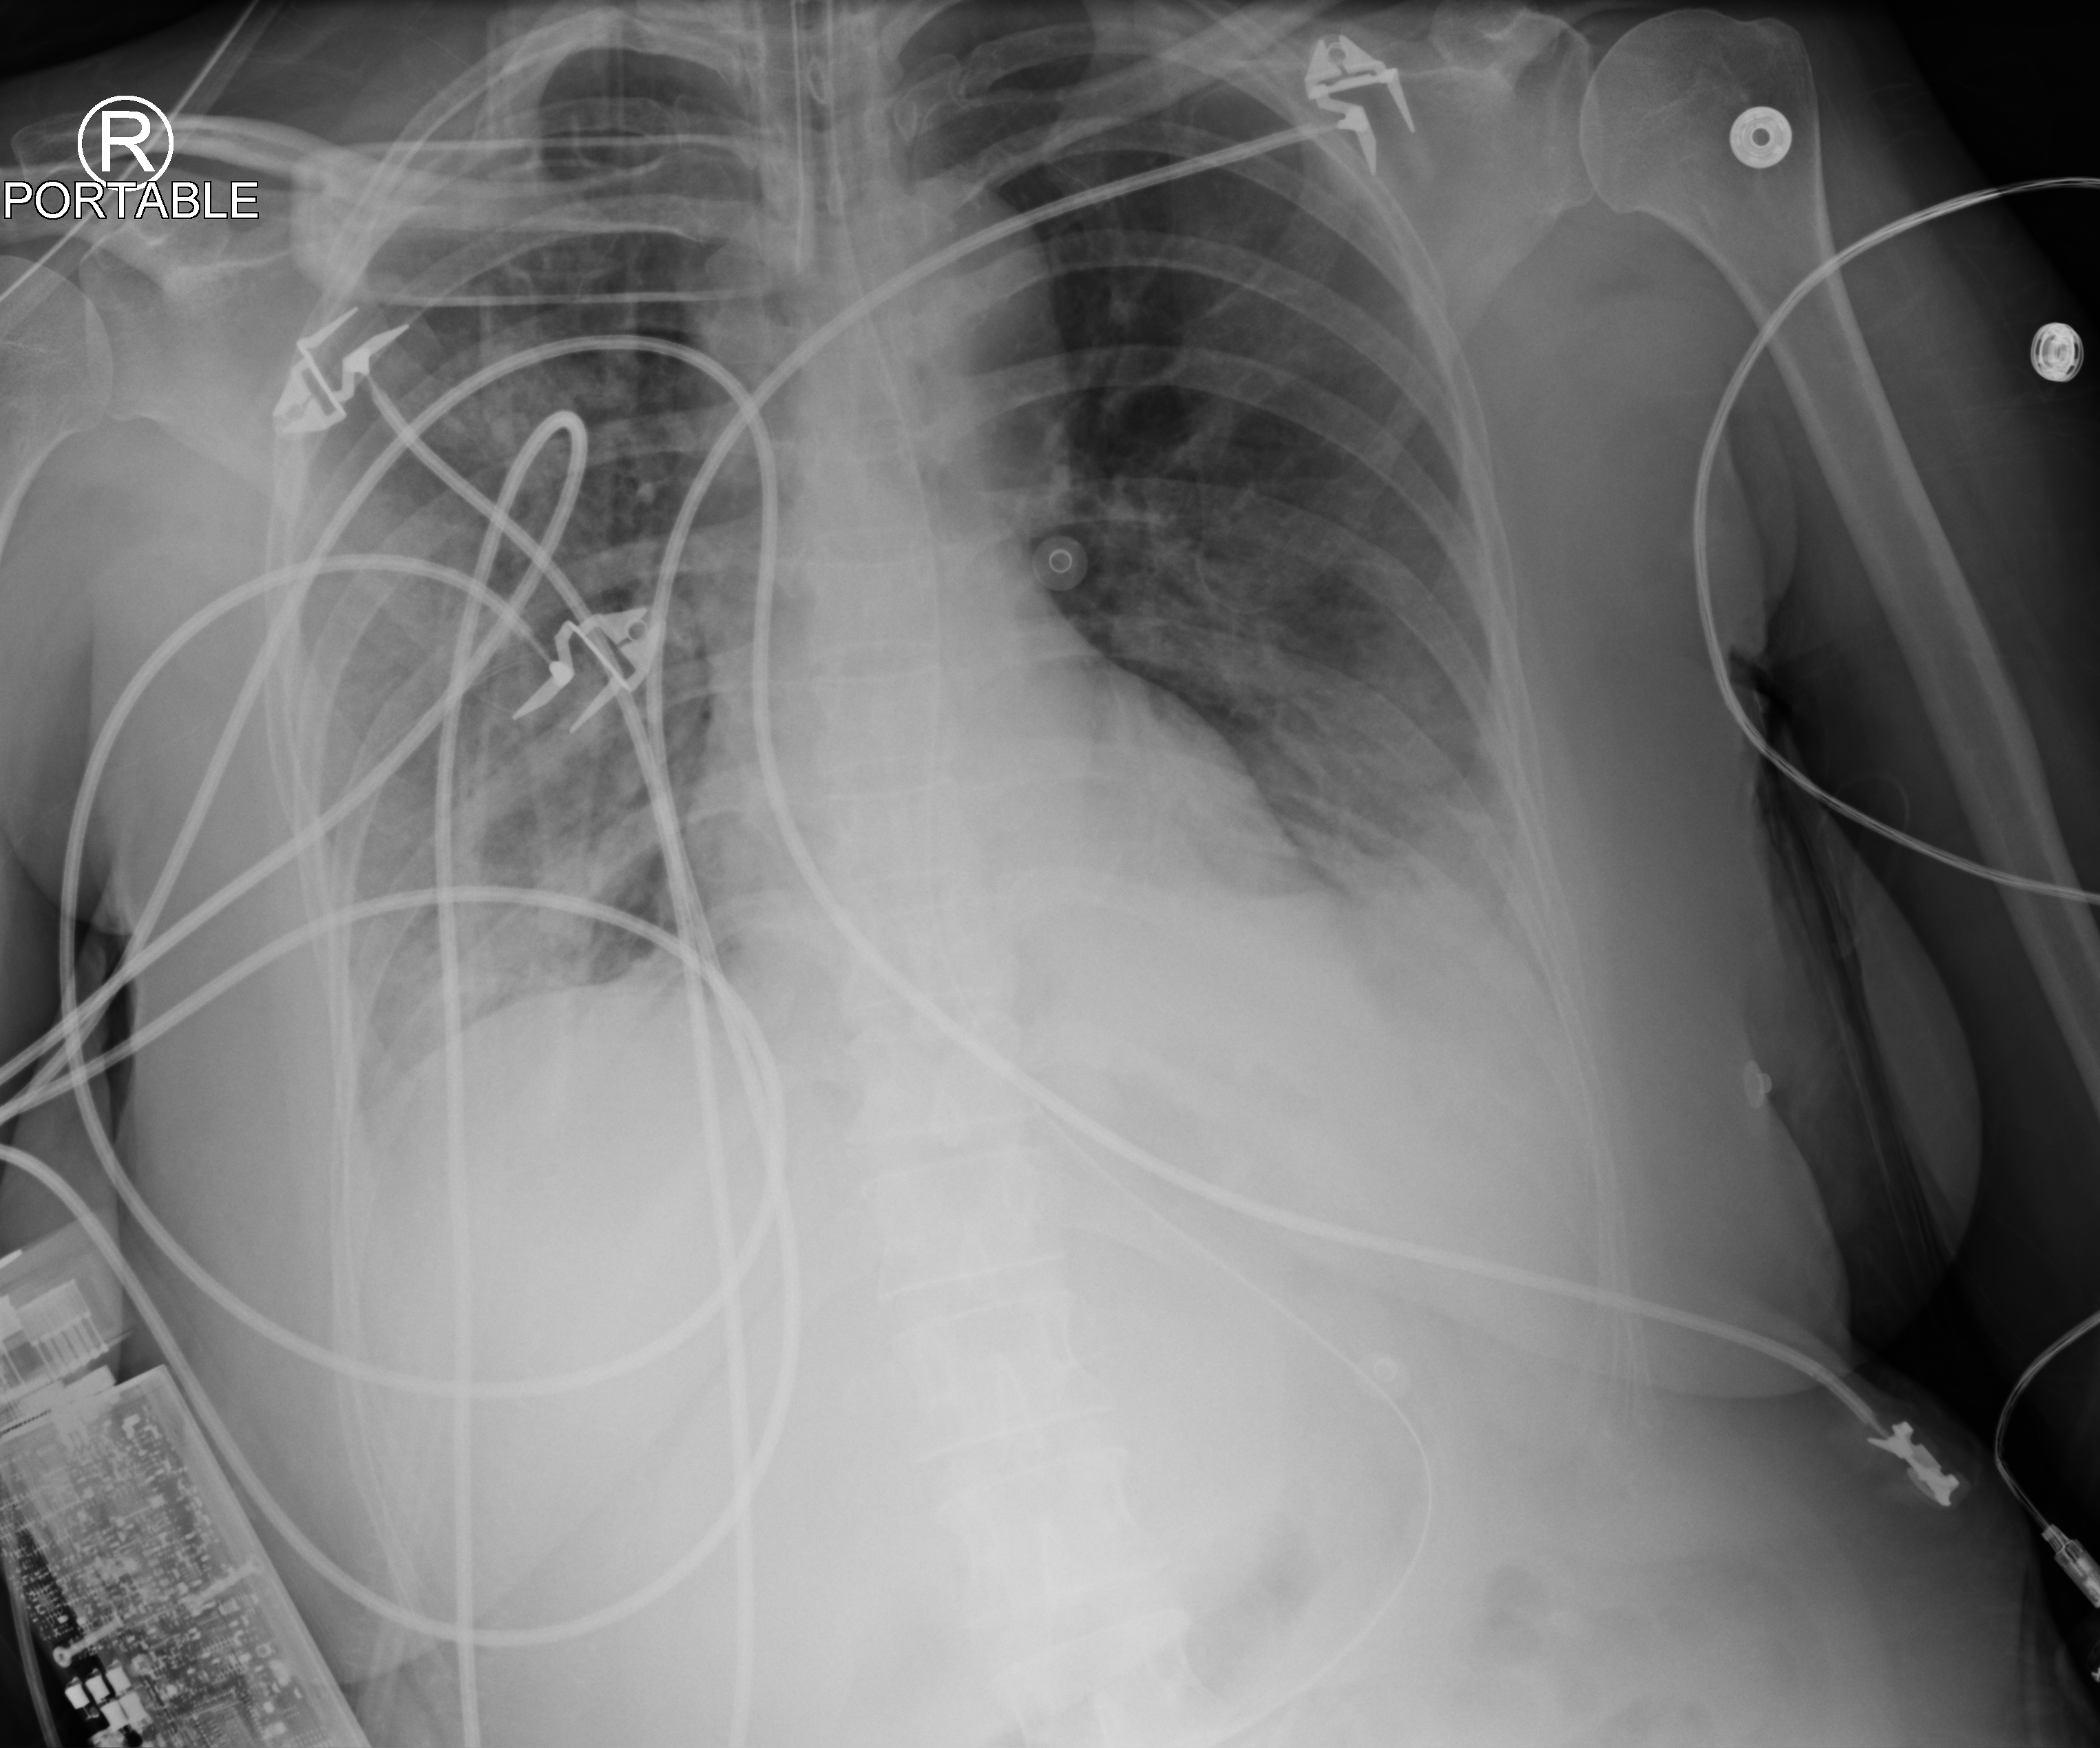
Chest X-ray (portable). Patient hospitalised with COVID-19; female, aged 18–59 years.
Hospital-stay facts (about this admission, not read from this image; timing relative to this image not recorded): mechanically ventilated during this hospital stay: yes; admitted to intensive care during this hospital stay: yes; diabetes (admission record): yes.